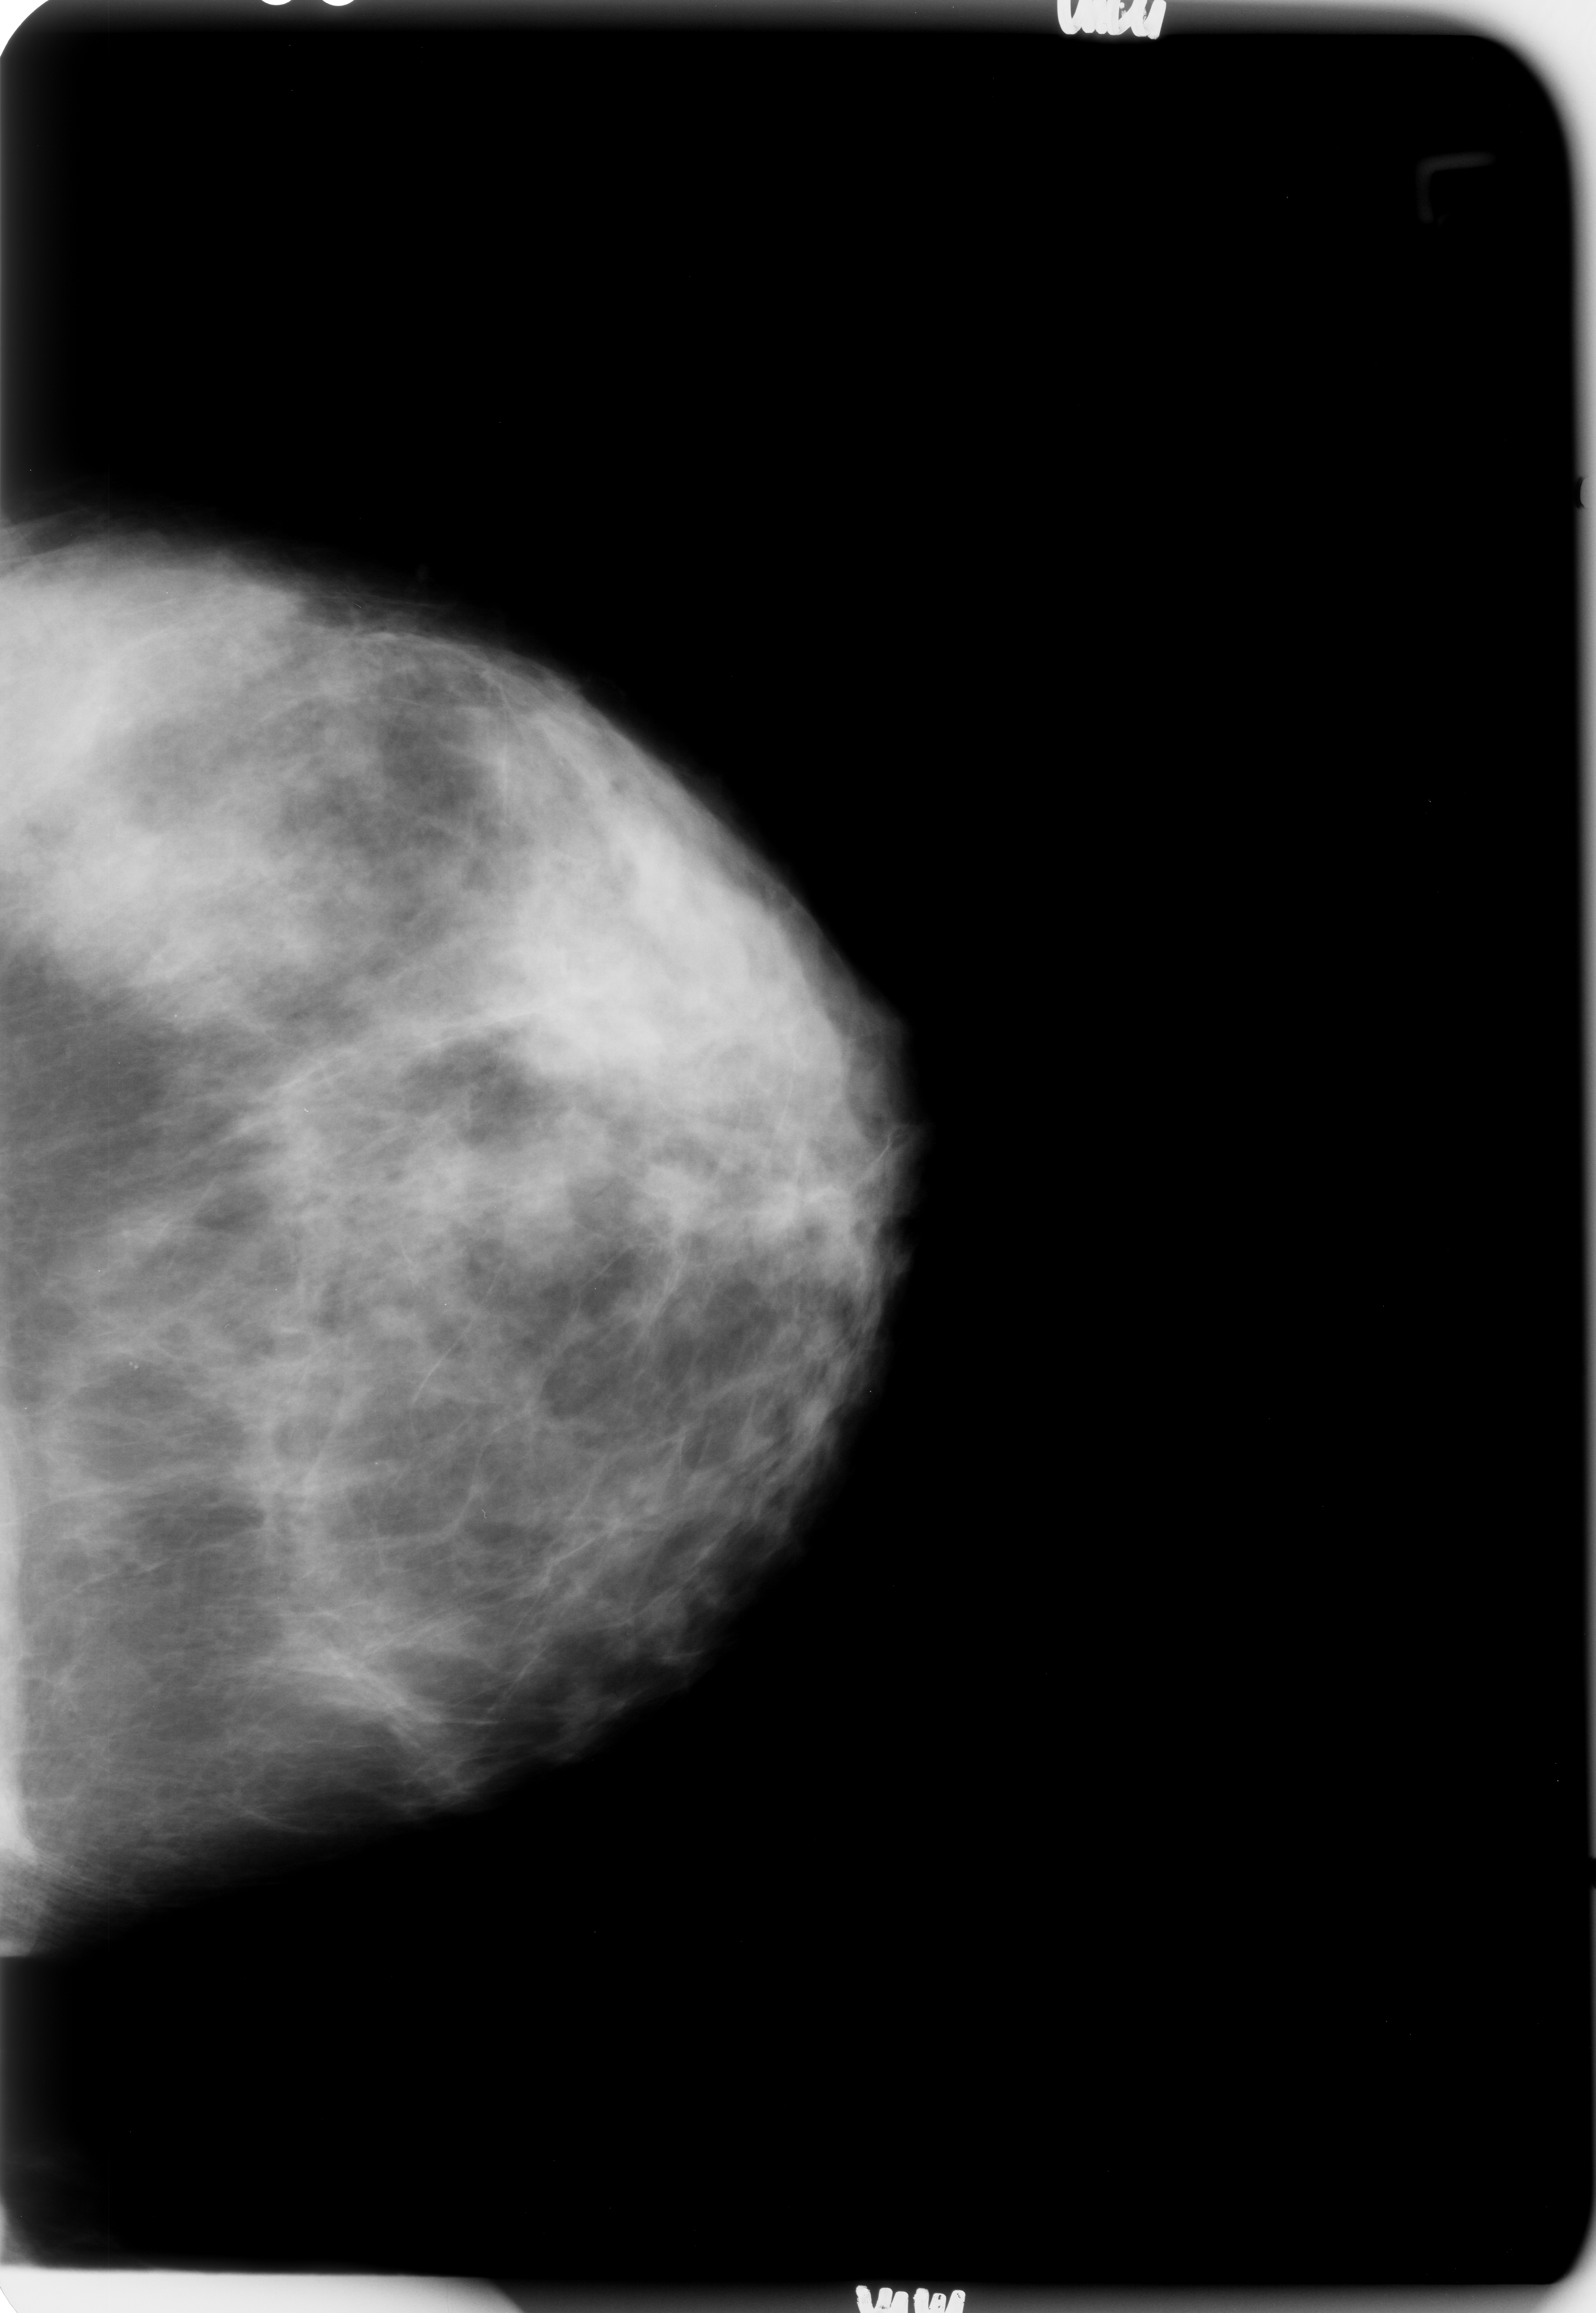
Digitized screen-film mammogram; left breast; craniocaudal (CC) view; BI-RADS breast density category 3 (scale 1–4); 1596 × 2313 image matrix.
Marked abnormalities (boxes around the expert regions of interest):
- calcifications, morphology amorphous / pleomorphic, distribution clustered; BI-RADS assessment category 4; subtlety rating 2 on a 1 (subtle) to 5 (obvious) scale; pathology (as recorded): malignant: box from (x=46, y=669) to (x=148, y=755) px